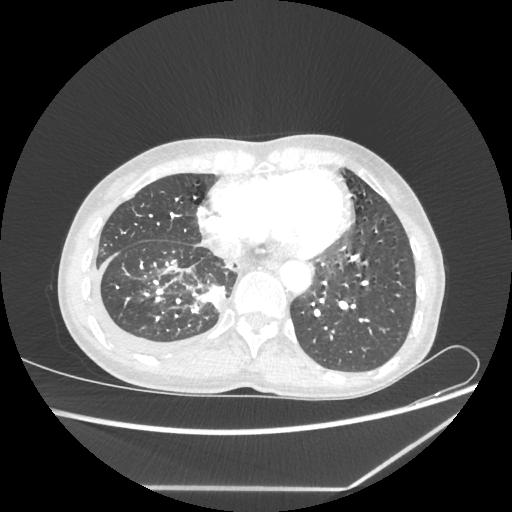
Chest CT, one axial slice. Slice 71 of 237 in the series (ordered by position). 80 kVp. Lung window (W 1500 / L -600 HU). 1.25 mm slice thickness. 512 × 512 image matrix. Female patient, age 59 years. From the clinical record (not read from this slice): clinical TNM (as recorded): T1c N1 M1.
Outlined on this slice (rectangle marked by the reading radiologist):
- lung tumour (recorded histology: adenocarcinoma): bounding box (x1, y1, x2, y2) in pixels: (204, 282, 228, 312)